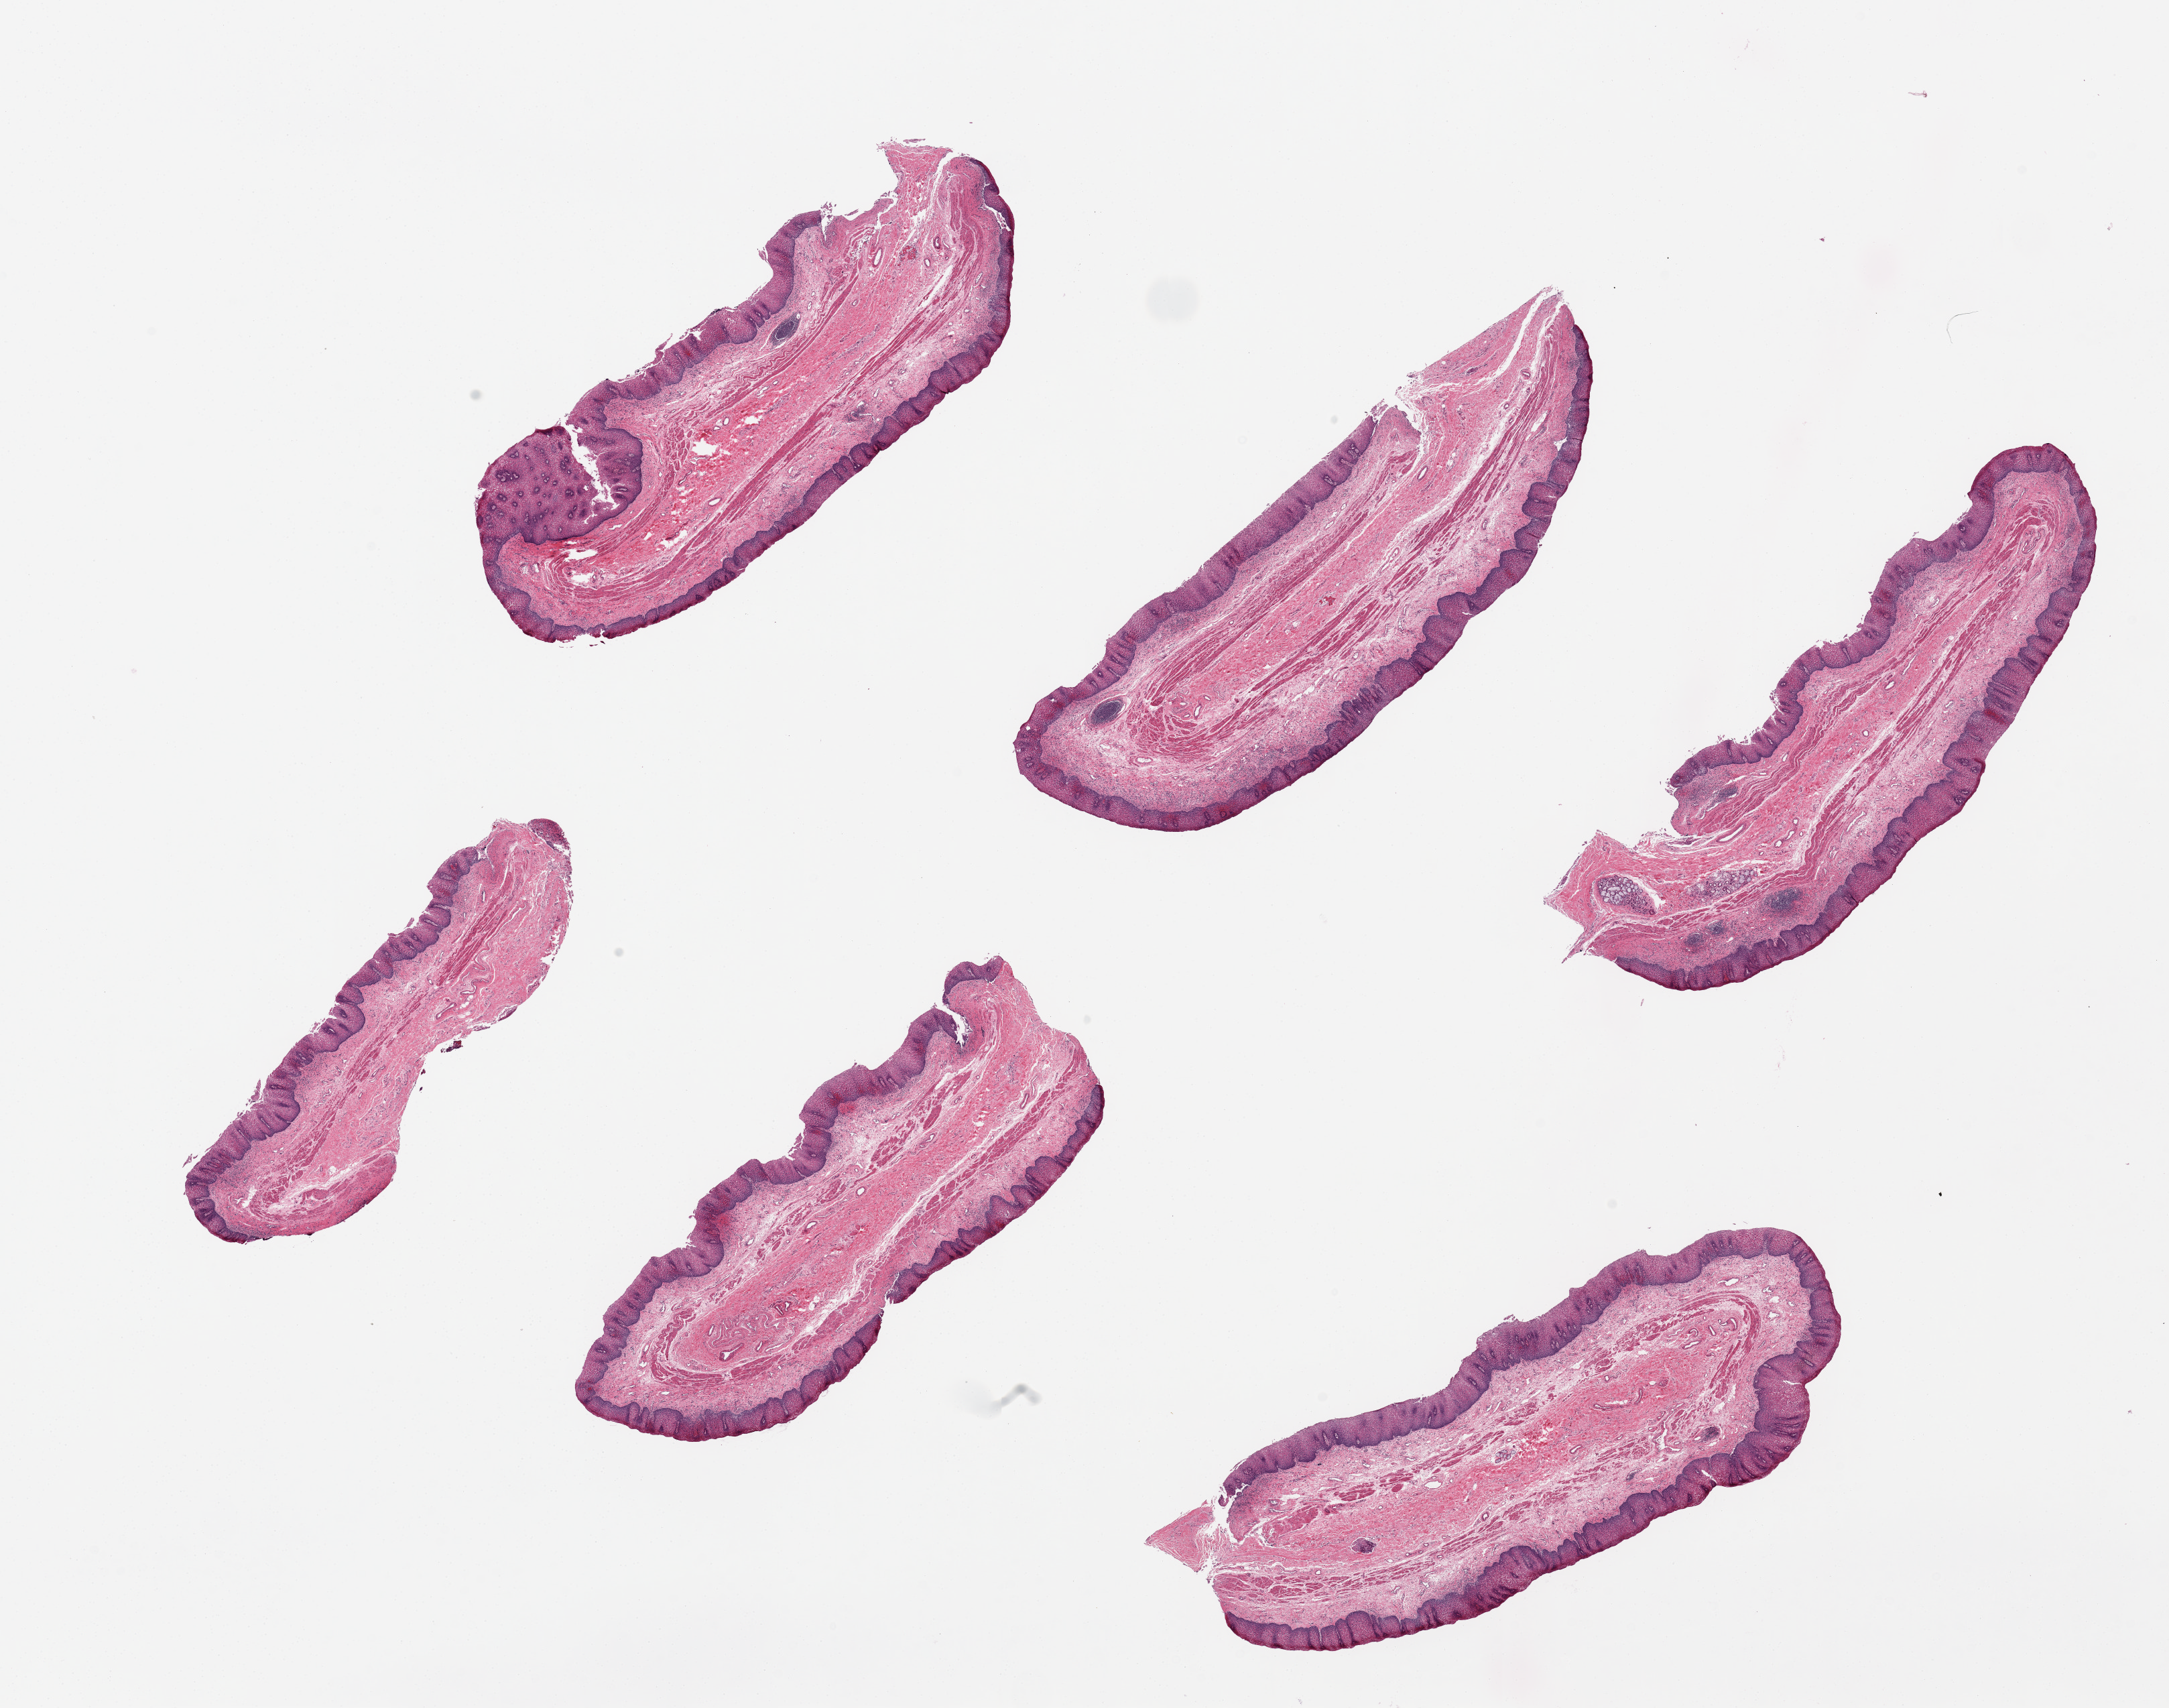
H&E whole-slide image — a low-resolution overview of the entire scanned area, about 25.6 x 20.2 mm; PAXgene-fixed paraffin-embedded (PFPE) section; sampled site (target tissue): esophageal mucous membrane; donor tissue sample. Donor: male.
Reviewer comment on this tissue sample: 6 pieces, esophagitis with erosion.